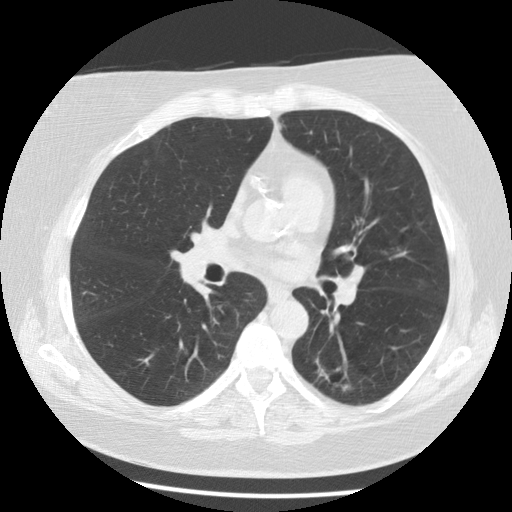
Chest CT (low-dose screening protocol), one axial image. Third screening round (two years after baseline). Lung window (W 1500 / L -600 HU). Slice 55 of 116 in the series. 512 × 512 image matrix, field of view 341 × 341 mm. Female participant, aged 59 years at enrolment. Current smoker at enrolment.
- Lesion marked by an expert reader, bounding box [x1, y1, x2, y2] px = [301, 349, 361, 408].
- The screening reader recorded 6 non-calcified nodules or masses ≥4 mm on this exam (right lower lobe, right upper lobe, right lower lobe, right lower lobe, left lower lobe, left lower lobe); which of them this box marks is not recorded.
- Official screen result: positive, other.
- Participant outcome: lung cancer diagnosed 56 days after this screen — adenocarcinoma, NOS, left lower lobe, poorly differentiated (G3), stage IA (AJCC 6th edition), 15 mm at pathology.